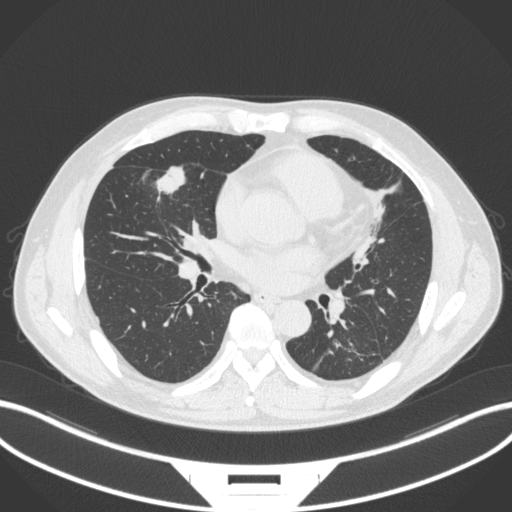
Chest CT, one axial slice; slice 147 of 399 in the series (ordered by position); reconstruction kernel B31f; lung window (W 1500 / L -600 HU); 1 mm slice thickness; 512 × 512 image matrix, field of view 400 × 400 mm. Male patient, age 59 years. Case-level facts recorded for this patient, not image findings: clinical TNM (as recorded): T2a N1 M0.
Structures marked on this image (bounding box drawn by a radiologist):
- lung tumour (recorded histology: adenocarcinoma): bounding box [x1, y1, x2, y2] px = [152, 162, 190, 200]